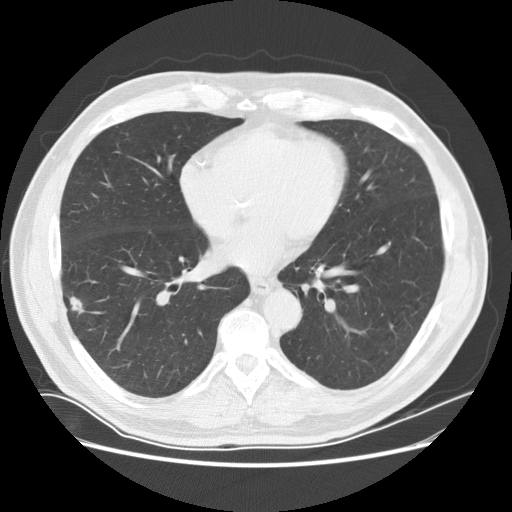
Low-dose screening chest CT, axial slice. Baseline screening round. Lung window (W 1500 / L -600 HU). Slice 95 of 170 in the series. Male participant, aged 72 years at enrolment. Current smoker at enrolment.
Expert reader's lesion annotation, bounding box <58,292,92,324> (left, top, right, bottom; pixels). The exam's reader record, not a measurement of the box and not confirmed to be the same lesion: non-calcified nodule or mass ≥4 mm, right lower lobe, 13 × 8 mm, poorly defined margins, soft tissue attenuation. Later outcome: lung cancer diagnosed 17 days after this screen — non-small cell carcinoma, right lower lobe, moderately differentiated (G2), stage IA (AJCC 6th edition), 10 mm at pathology.